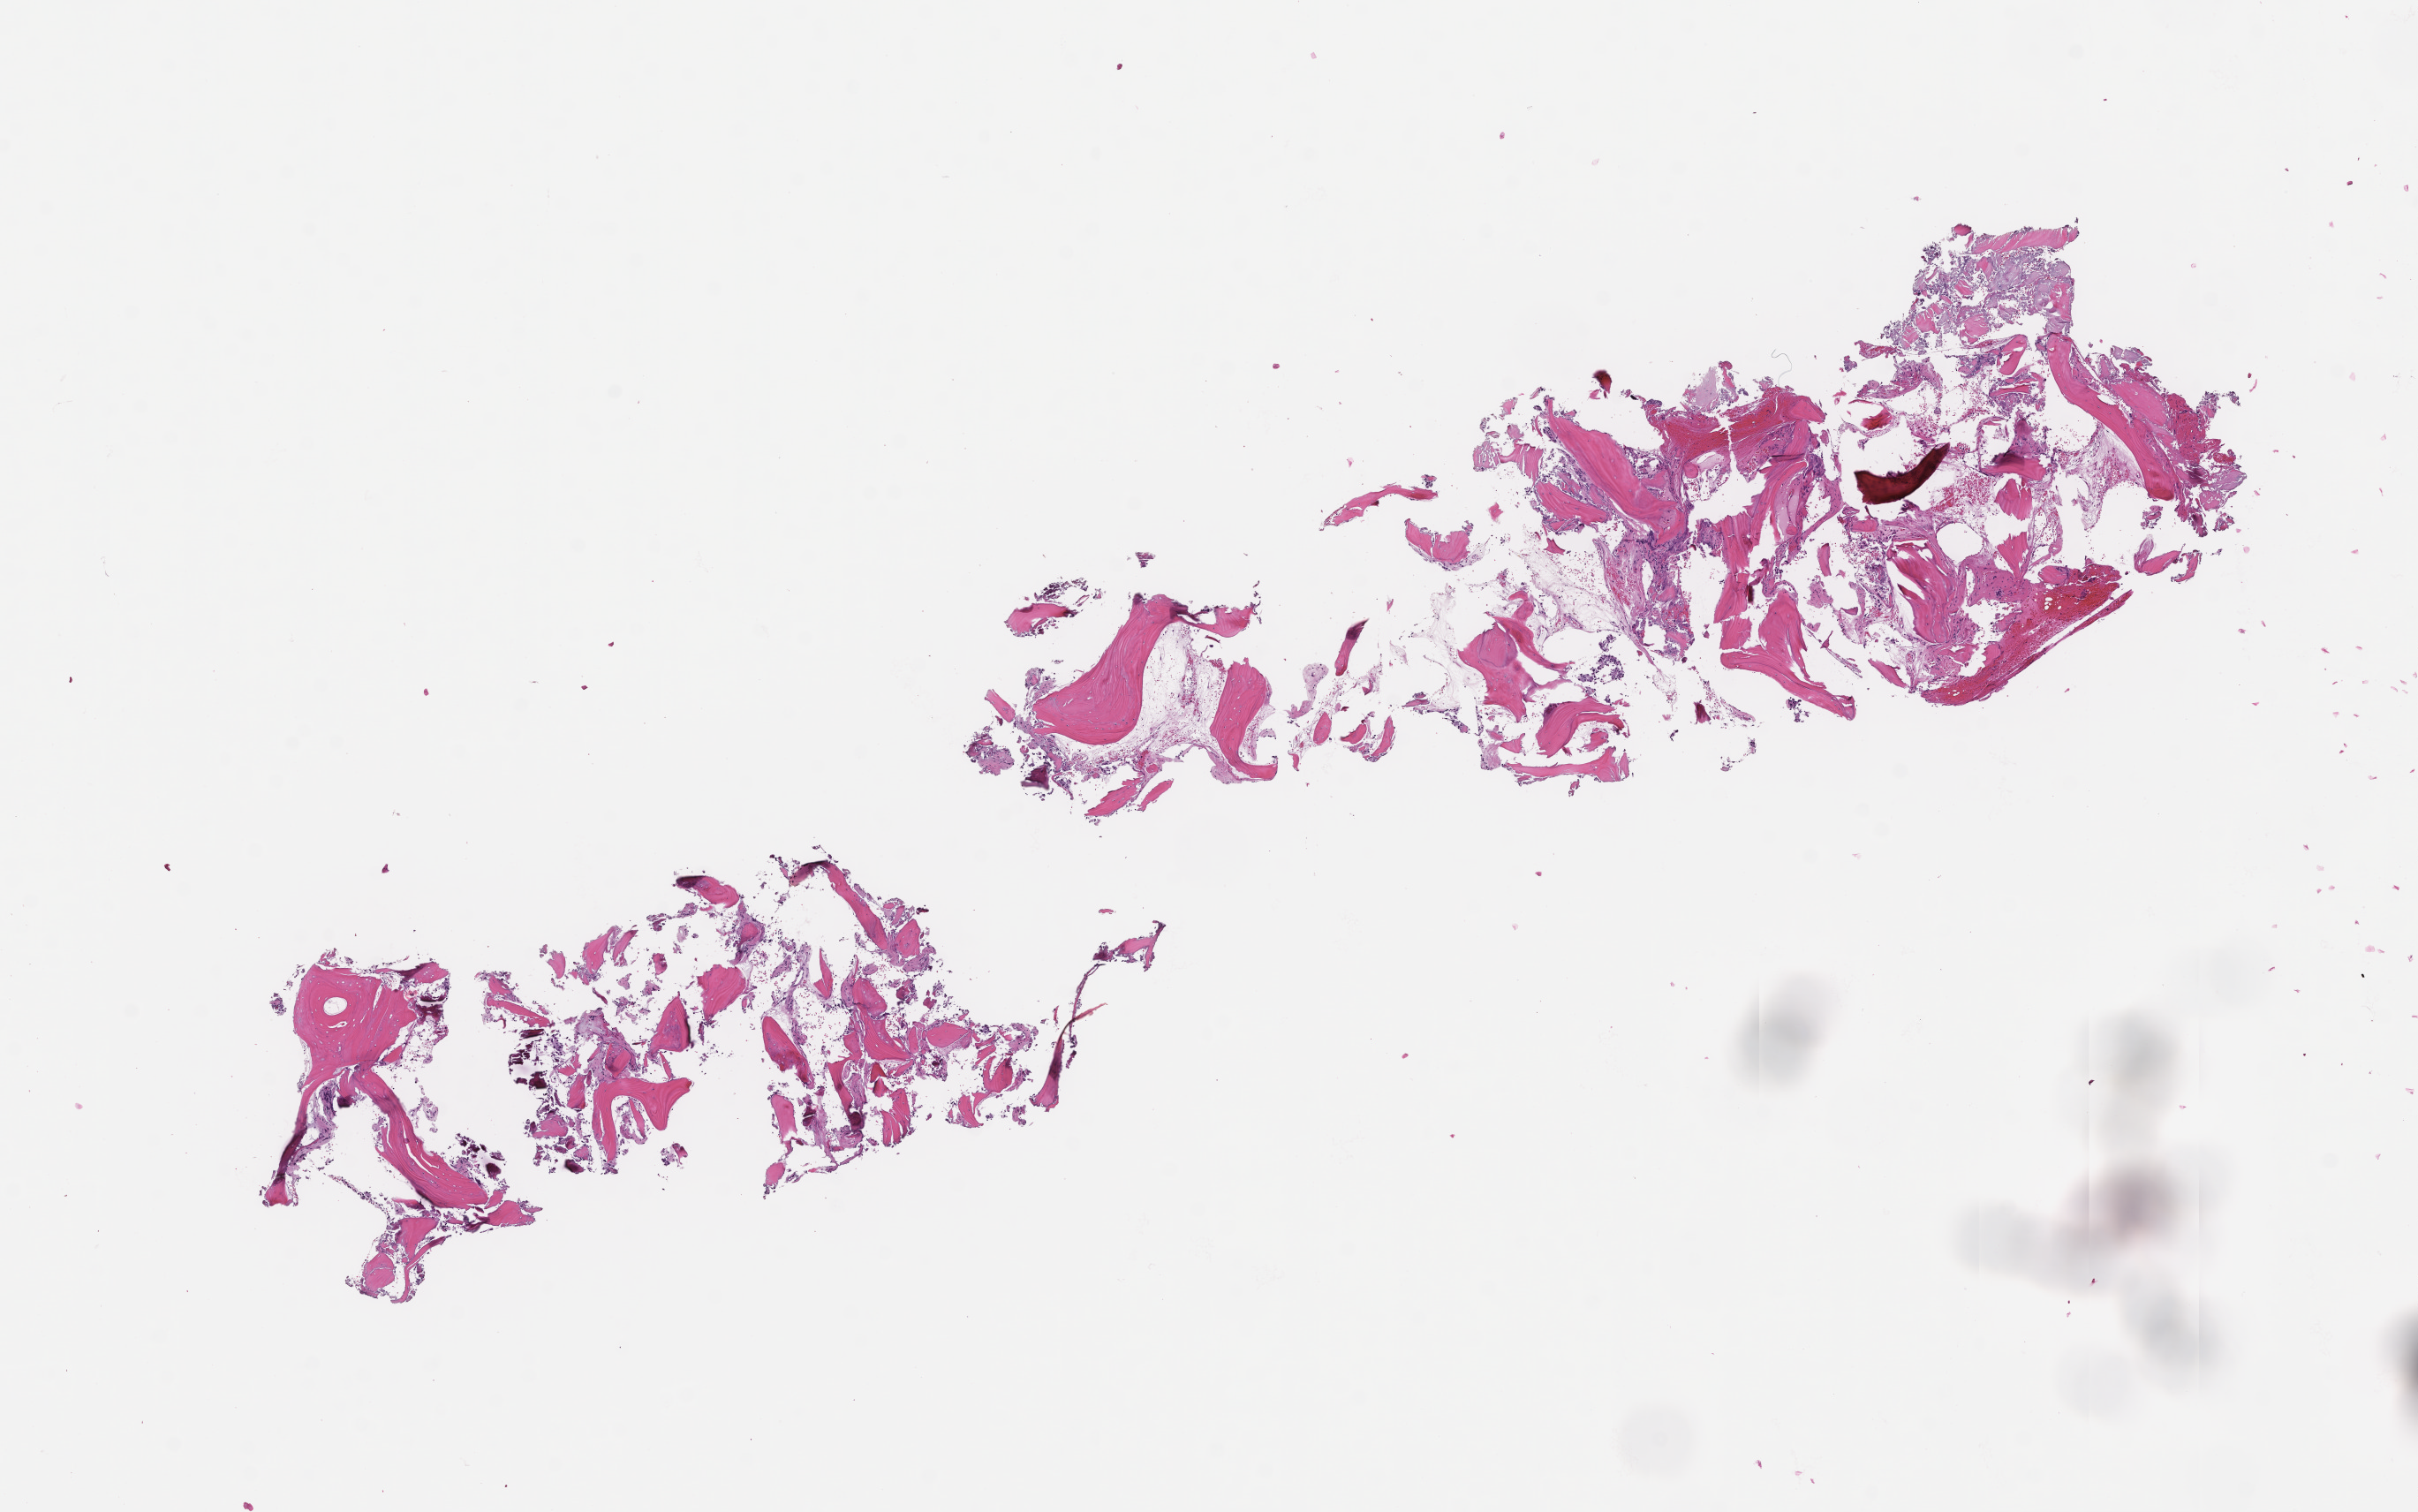
Digitized haematoxylin and eosin-stained section — whole scanned area (about 11.1 x 6.9 mm) shown as a low-resolution overview, formalin-fixed, paraffin-embedded (FFPE) tissue. Male patient.
• this section: metastasis (sampled organ not recorded)
• primary diagnosis of the patient: Prostate Carcinoma